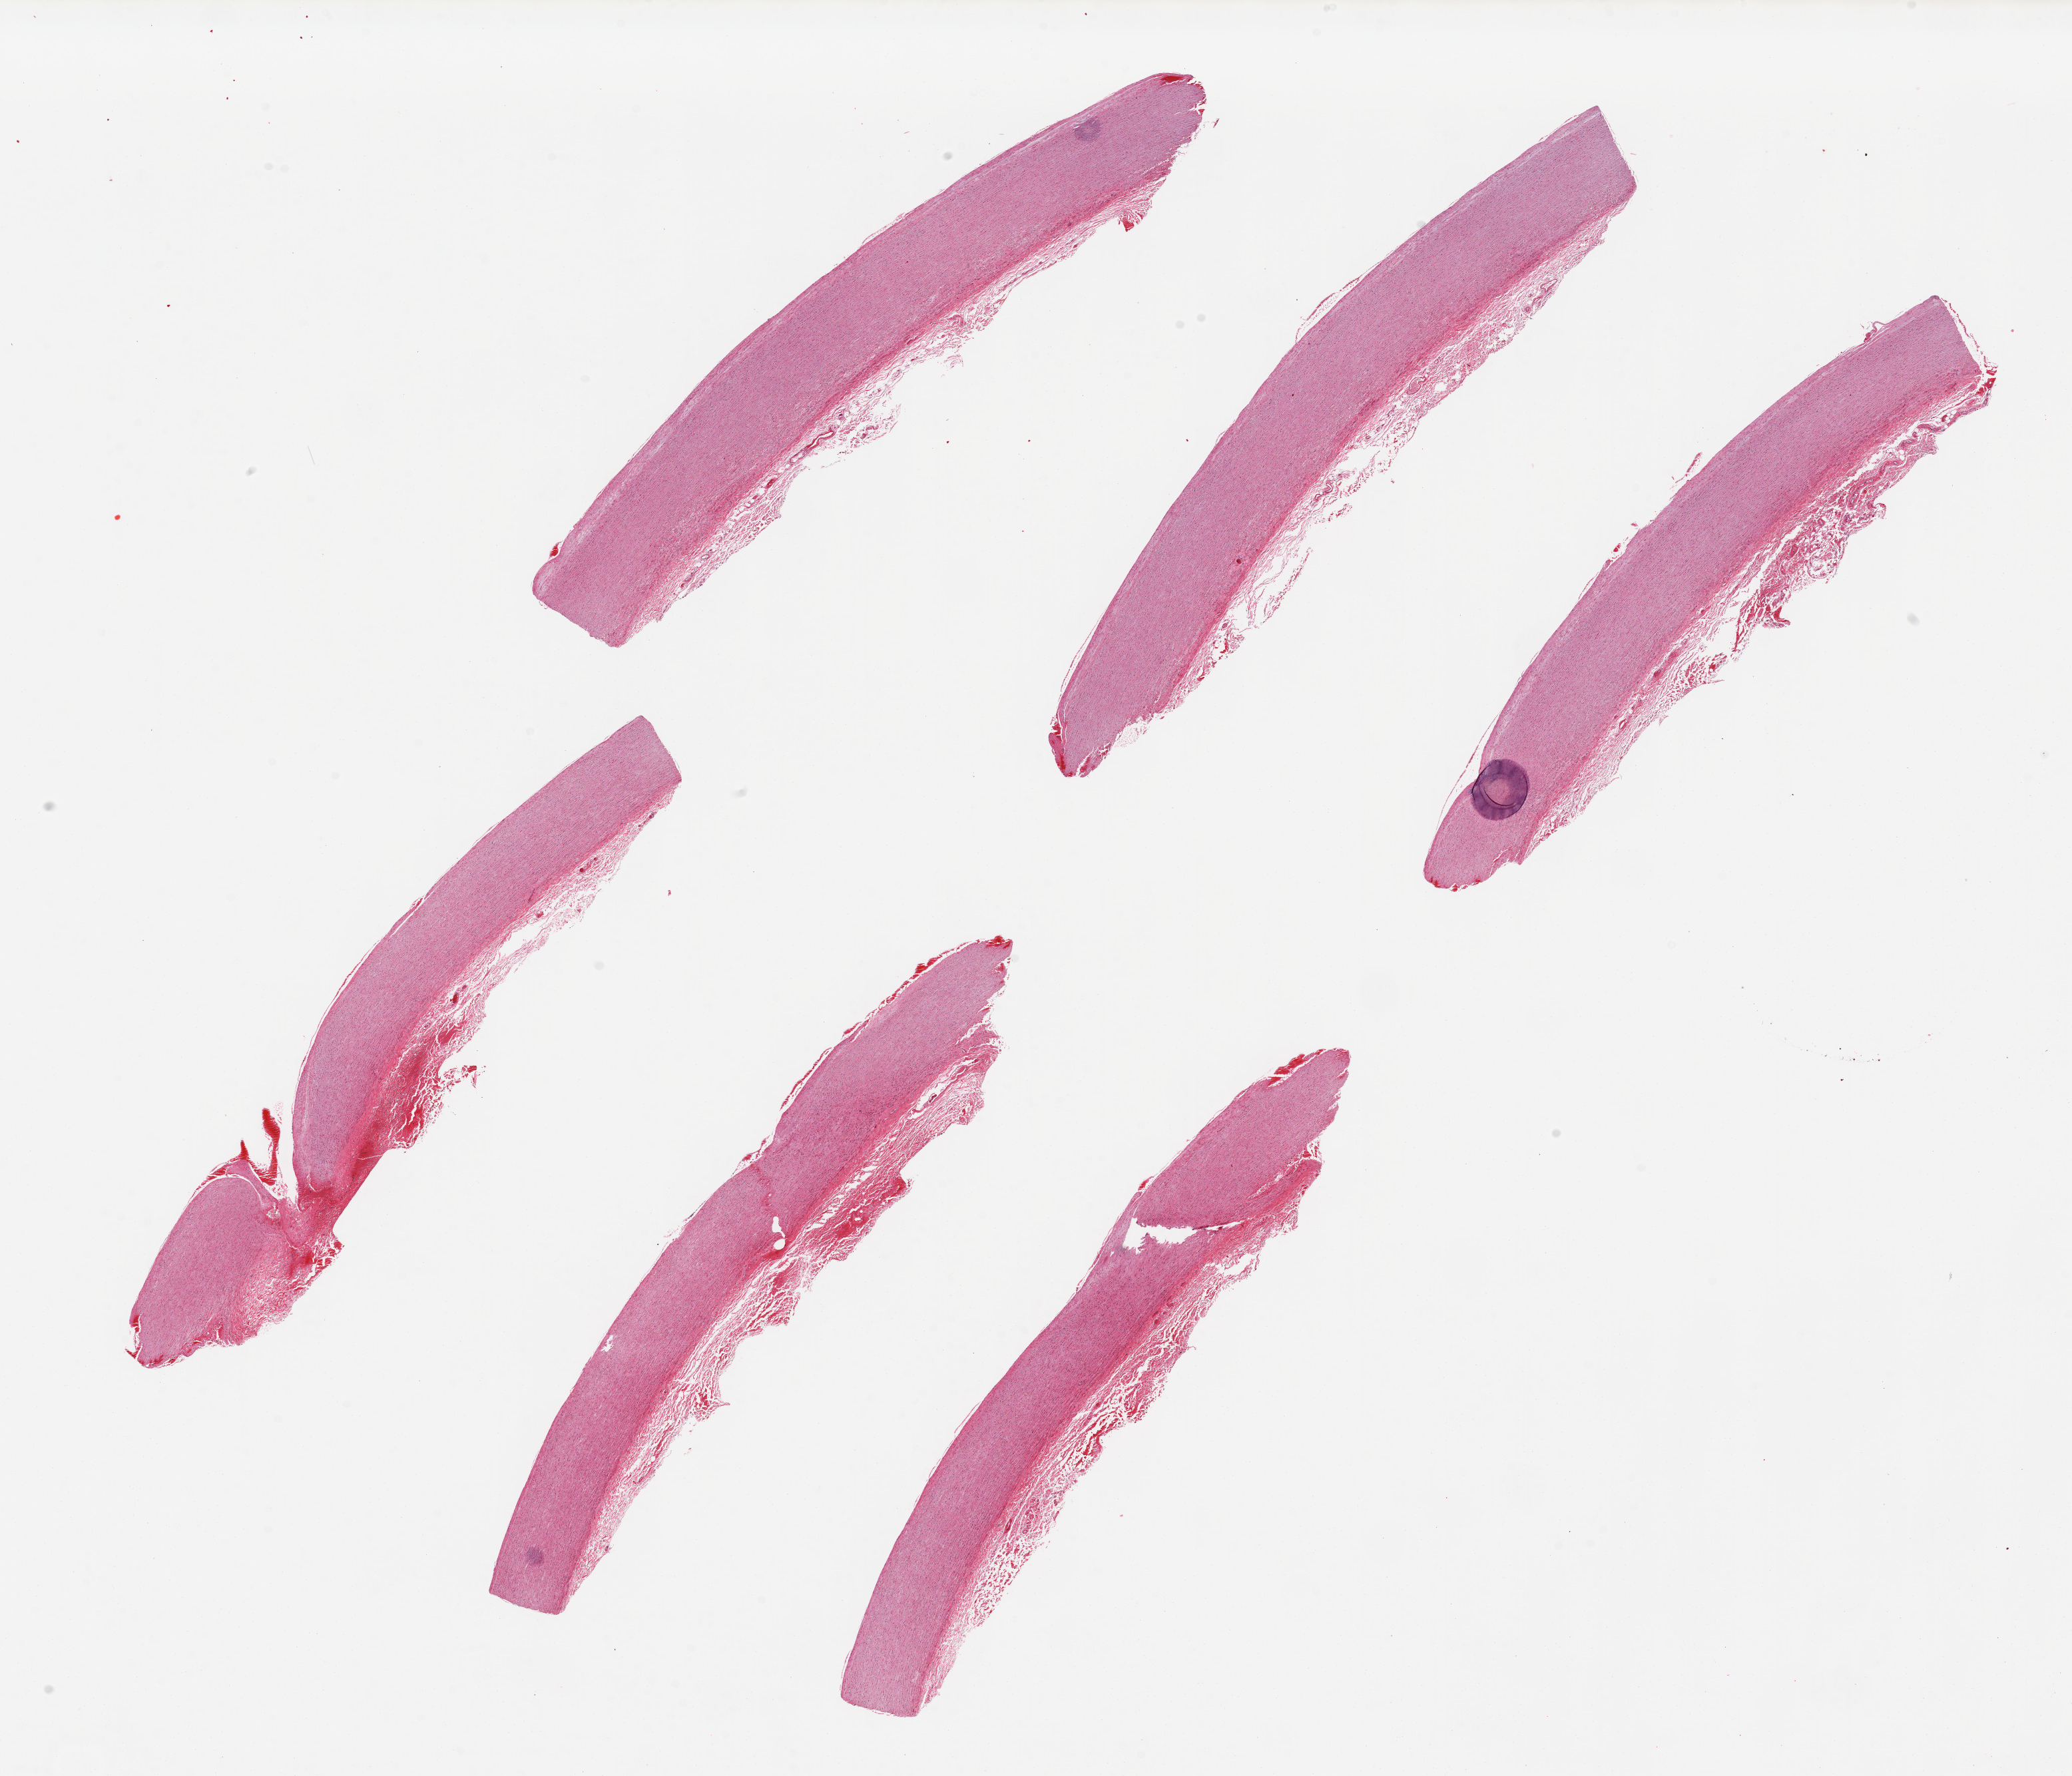
Digitized hematoxylin and eosin (H&E)-stained section — a low-resolution overview of the entire scanned area, about 24.6 x 21.1 mm (slide scanned at 20x), PAXgene-fixed, paraffin-embedded tissue, target tissue: aorta, tissue donor sample. Donor sex: female.
* review note (as recorded): 6 pieces up to 10x1.7 mm; minimal intimal sclerosis